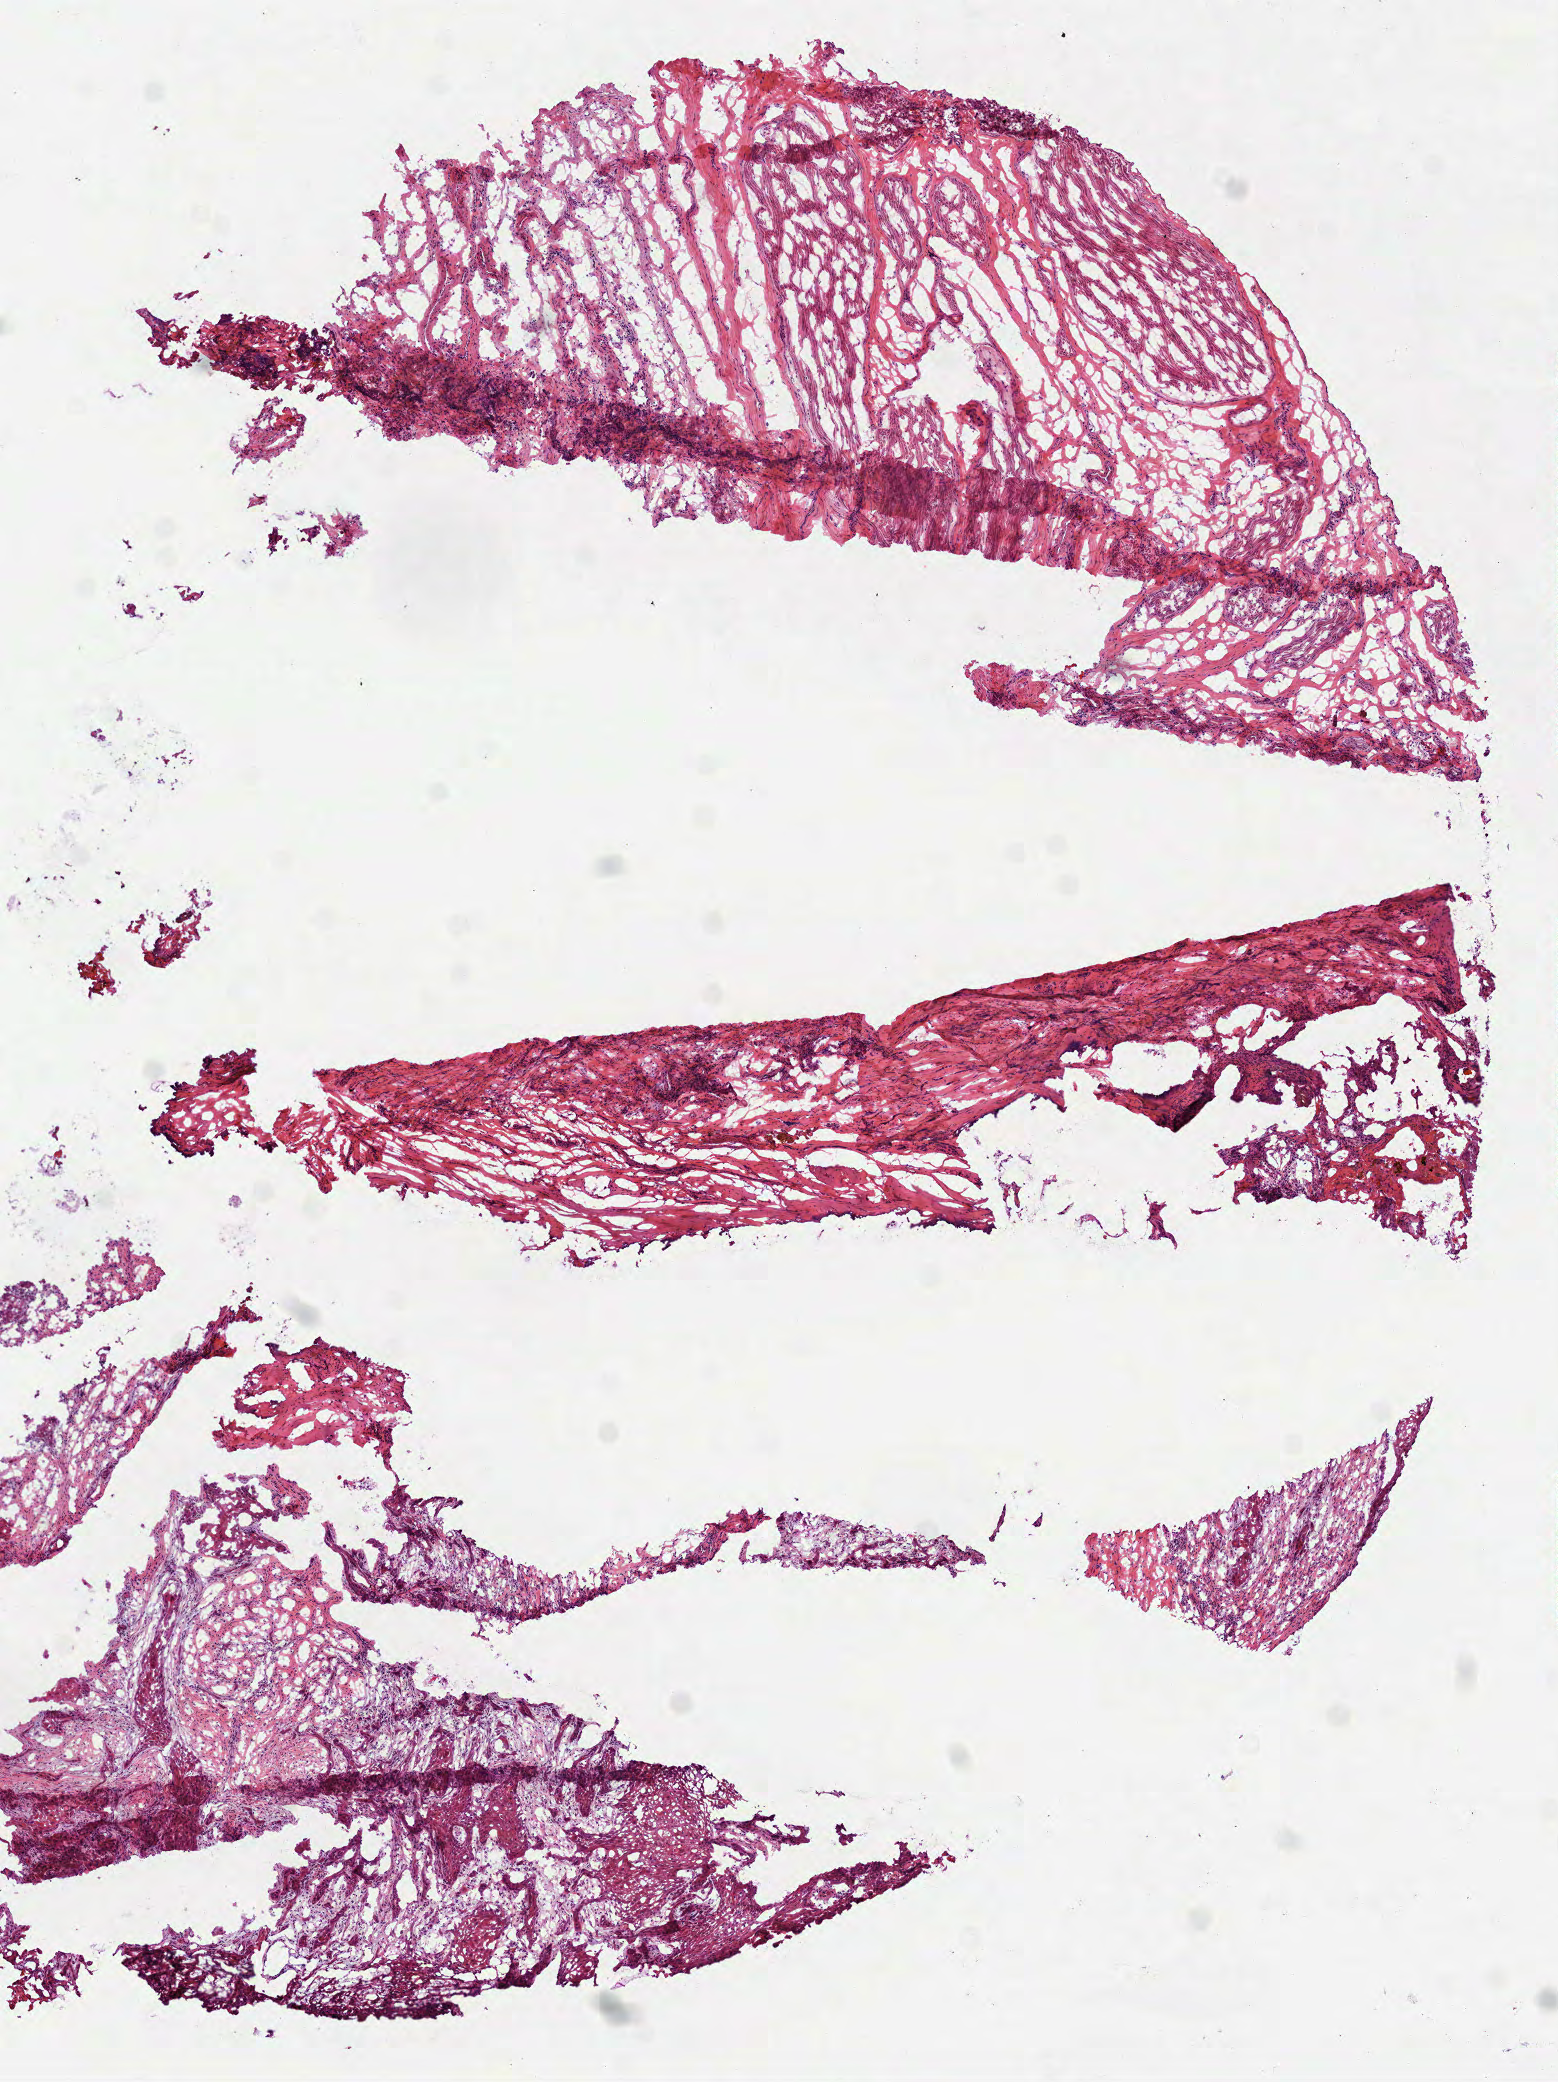
Hematoxylin and eosin (H&E) stained whole-slide image, low-resolution overview of the scanned area, about 6.3 x 8.4 mm (slide scanned at 40x); frozen section; primary tumour sample from the head and neck. Female patient; age at initial diagnosis 77 years. Pathologist review of this section (percent, as recorded): tumour cells 30%, tumour nuclei 50%.
Pathologic diagnosis: Squamous cell carcinoma, NOS (tongue, NOS).